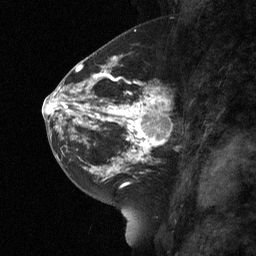
Breast MRI (dynamic contrast-enhanced), one sagittal slice; slice 33 of 64 in the series (ordered by position); dynamic contrast-enhanced study with each time point stored as its own series, time point 2 of 3 at this slice position (early post-contrast, ordered by acquisition time); 1.5 T; TE 4.8 ms, TR 27 ms; 256 × 256 image matrix, field of view 180 × 180 mm. Female patient, age 42 years. From the clinical record (not read from this slice): setting: breast cancer imaged before/during neoadjuvant chemotherapy; receptor status: triple-negative.
Annotated regions visible in this slice (semi-automatically segmented with operator editing):
- analysis volume of interest (the breast-tissue region the enhancement analysis was run in; not a lesion): bounding box <115,85,187,160> (left, top, right, bottom; pixels)
- tumour enhancement mask (voxels above the 90 % enhancement threshold inside the analysis volume of interest): <115,85,170,160>